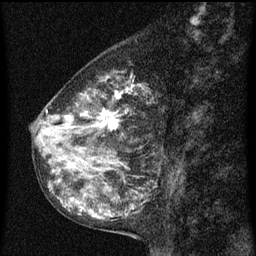
Breast MRI (dynamic contrast-enhanced), one sagittal slice. Slice 30 of 60 in the series (ordered by position). Dynamic contrast-enhanced series, image 2 of 3 at this slice position (ordered by acquisition). 1.5 T. TE 4.2 ms, TR 8 ms. 2 mm slice thickness. 256 × 256 image matrix. Female patient, age 55 years.
Annotated regions visible in this slice (semi-automatic segmentation, software-assisted and operator-edited):
- analysis volume of interest (the breast-tissue region the enhancement analysis was run in; not a lesion): bounding box [x1, y1, x2, y2] px = [34, 72, 157, 151]
- tumour enhancement mask (voxels above the 70 % enhancement threshold inside the analysis volume of interest): [48, 78, 135, 137]